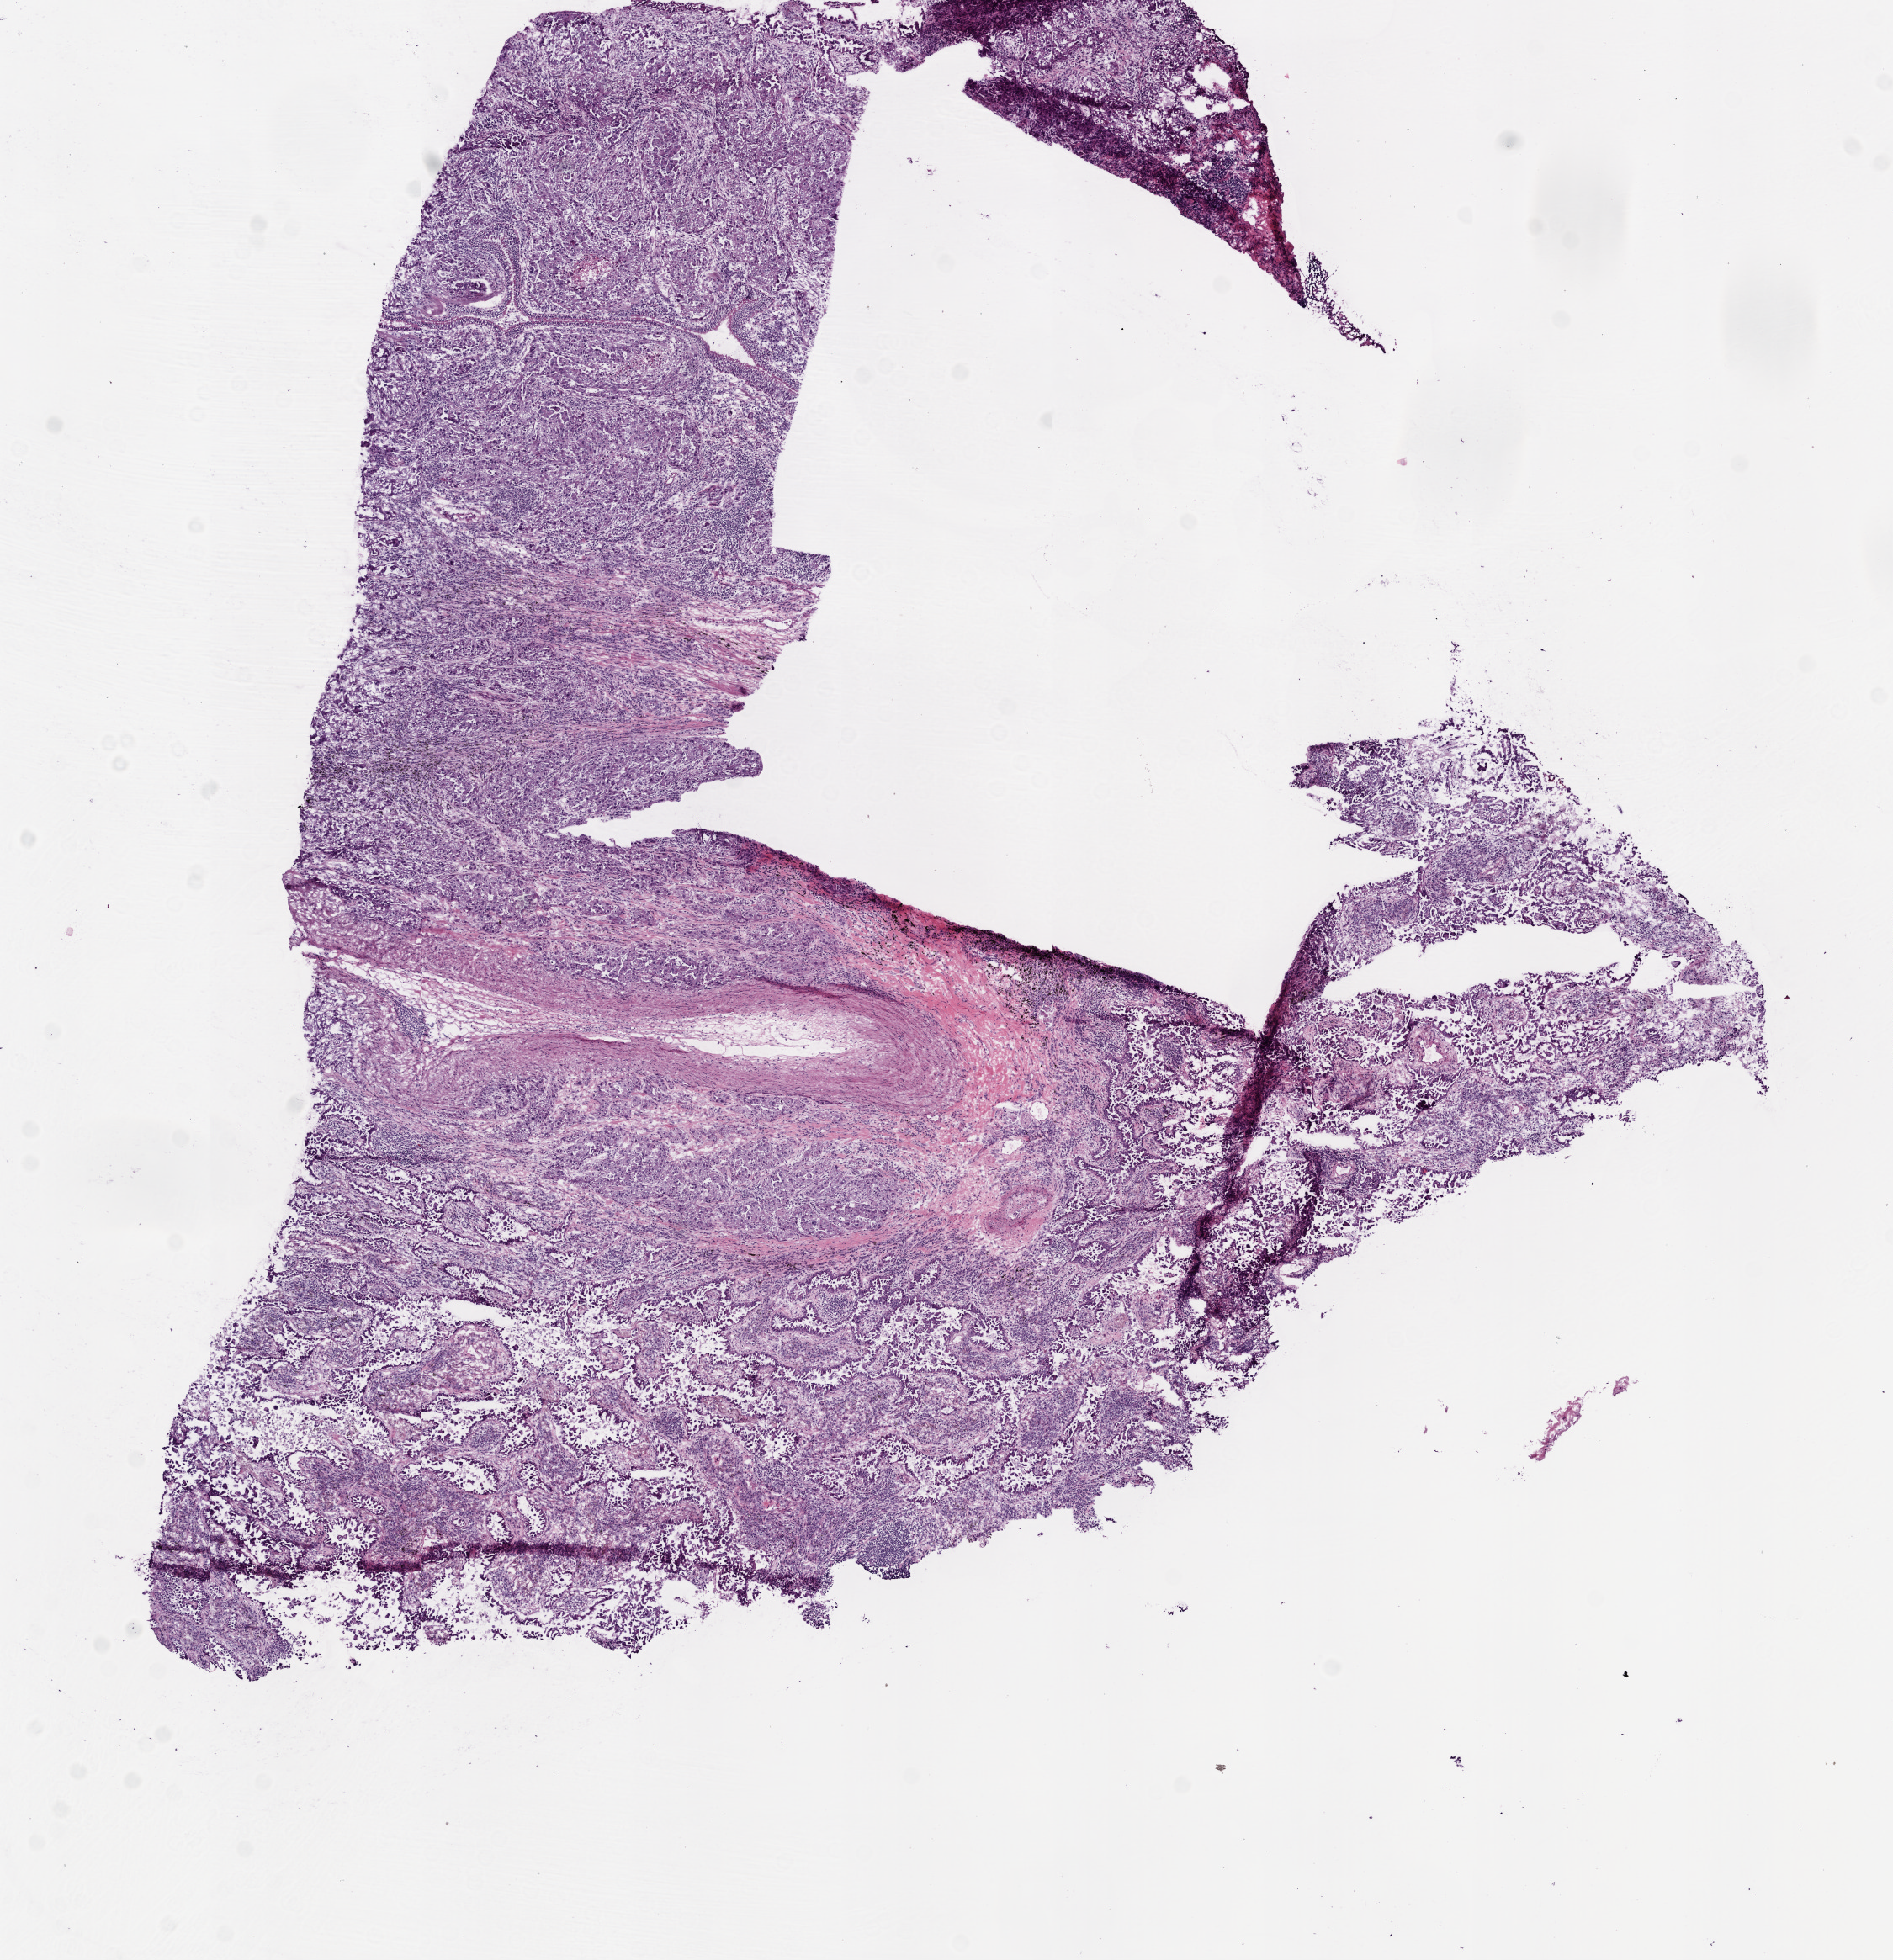
Hematoxylin and eosin (H&E) stained whole-slide image — shown as a low-resolution overview of the whole scanned area (about 9.0 x 9.3 mm, acquisition: 20x scan); frozen section; primary tumour sample from the lung. Male, age 62 years at initial diagnosis.
Pathologic diagnosis: Adenocarcinoma with mixed subtypes (upper lobe, lung).